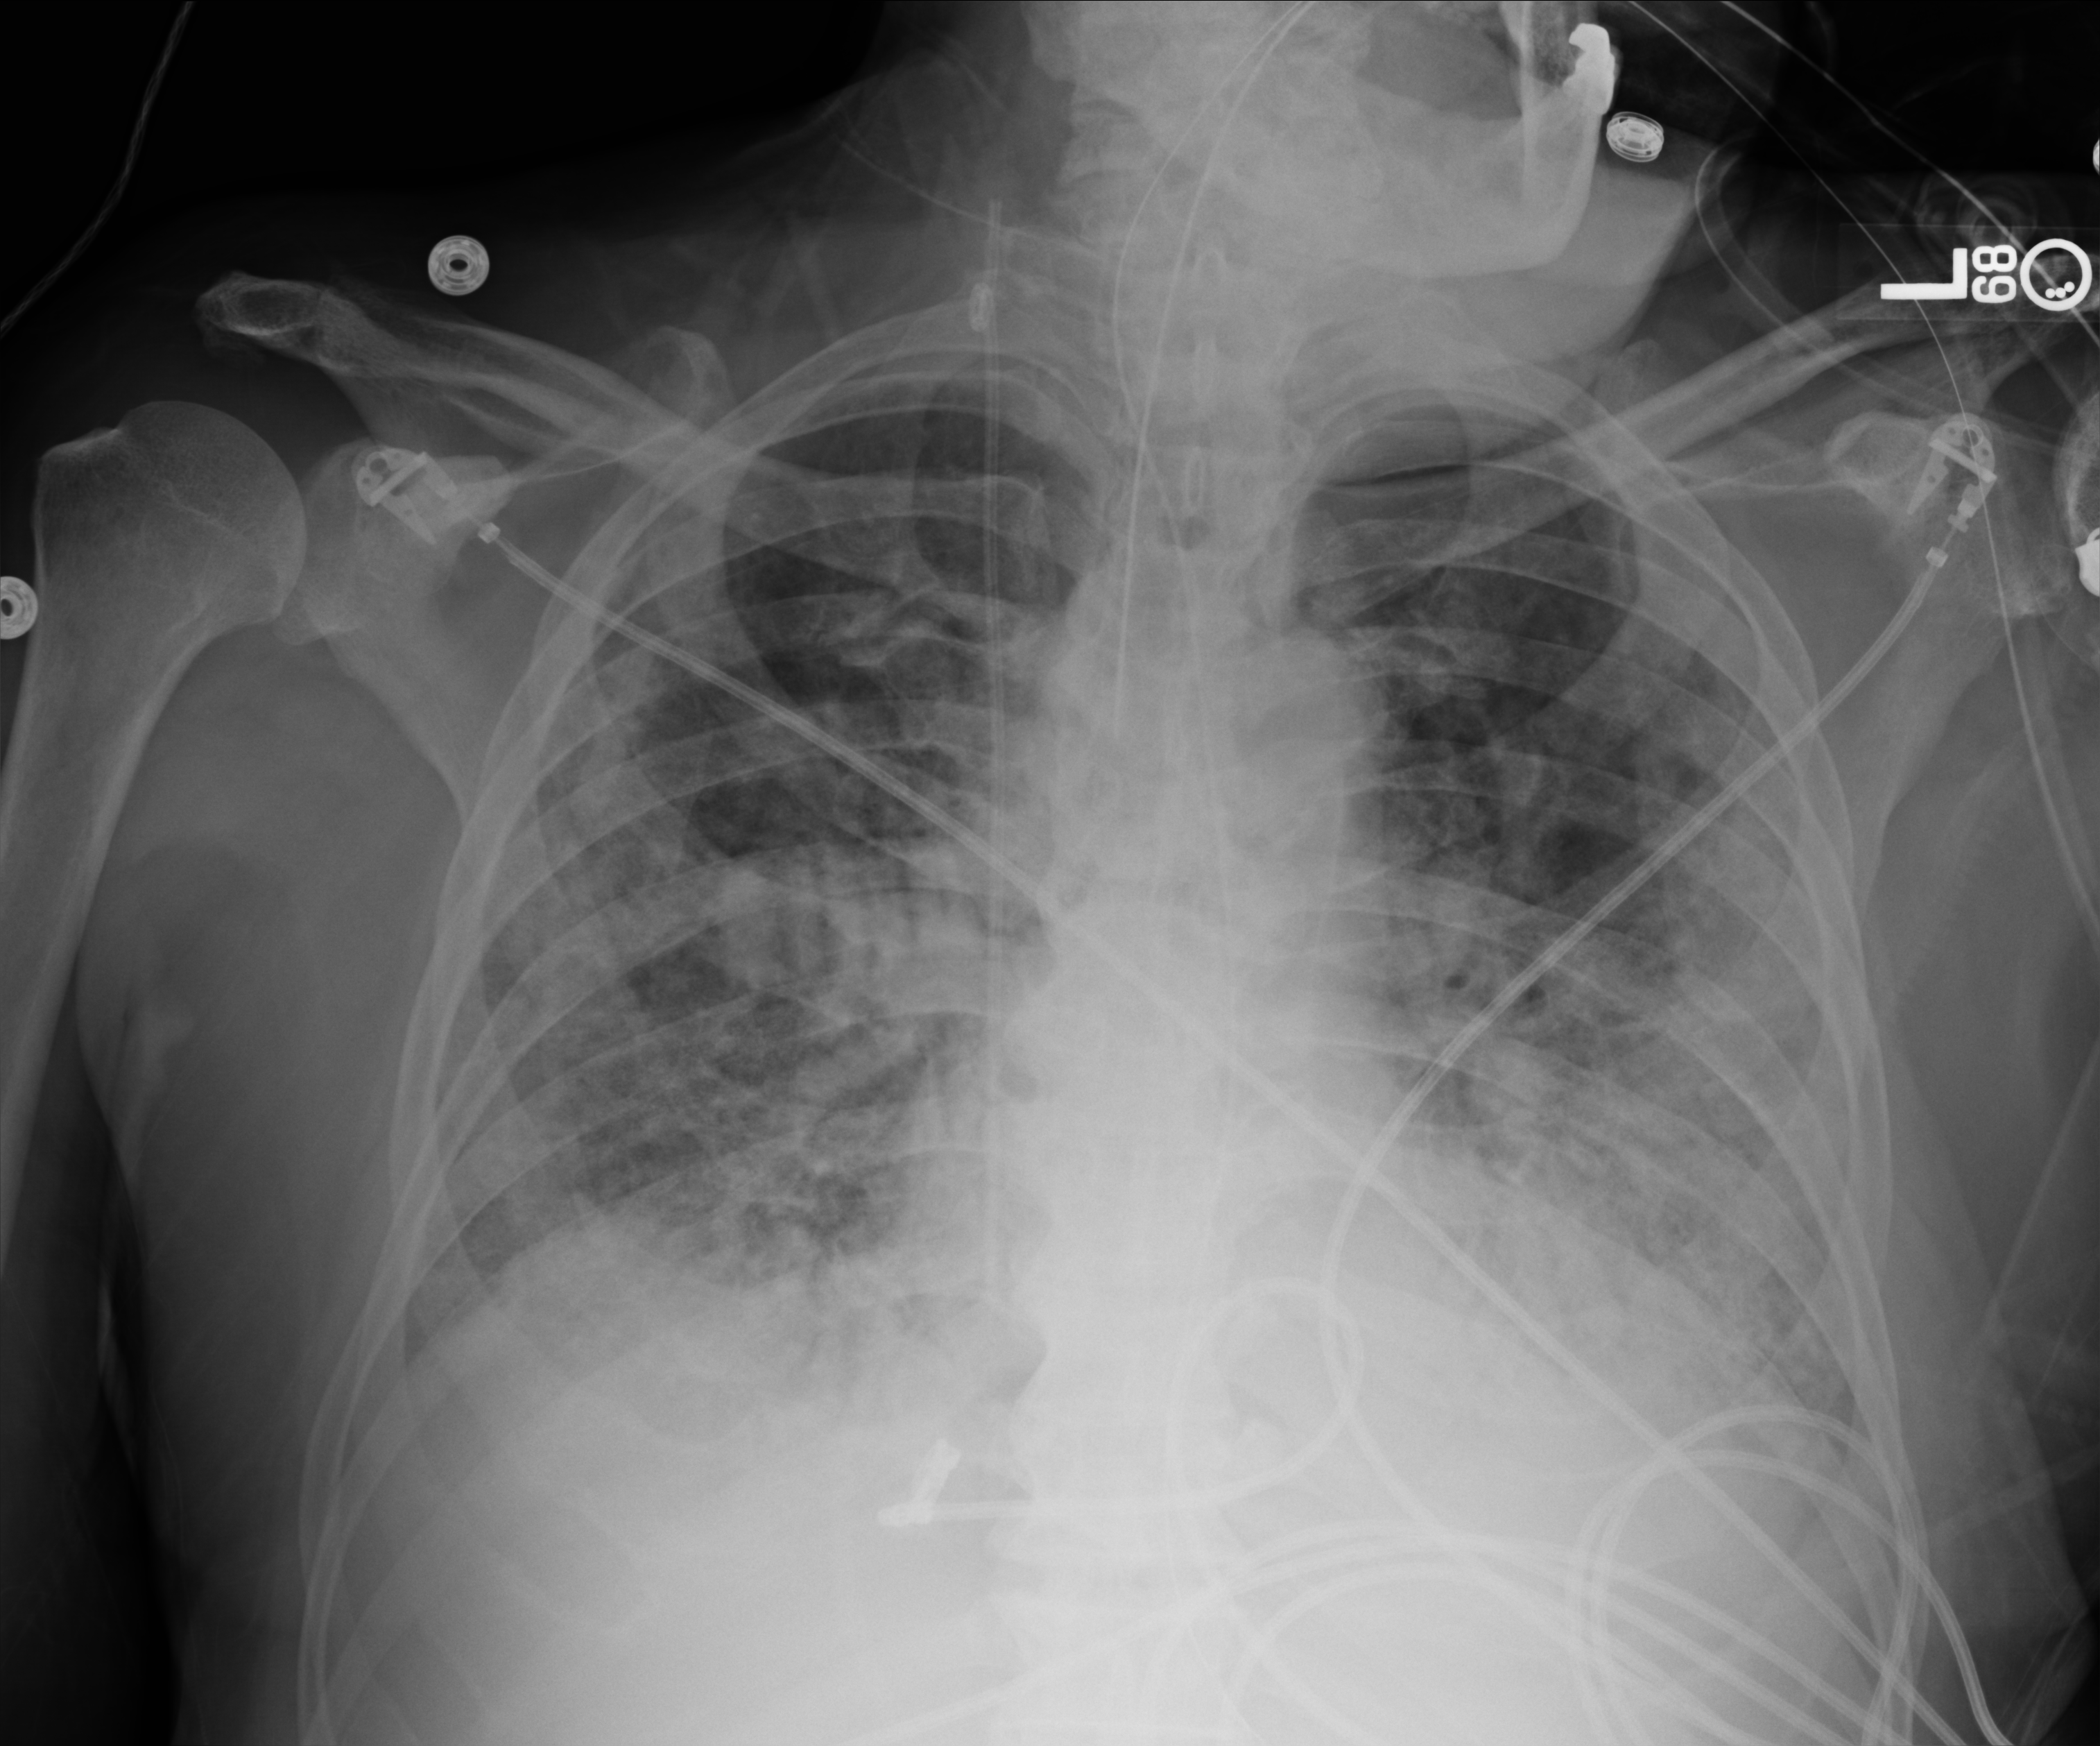
Chest X-ray (portable); anteroposterior (AP) projection. Male patient hospitalised with COVID-19, age 75–90 years.
Hospital-stay facts (about this admission, not read from this image; timing relative to this image not recorded):
- length of hospital stay: 33 days